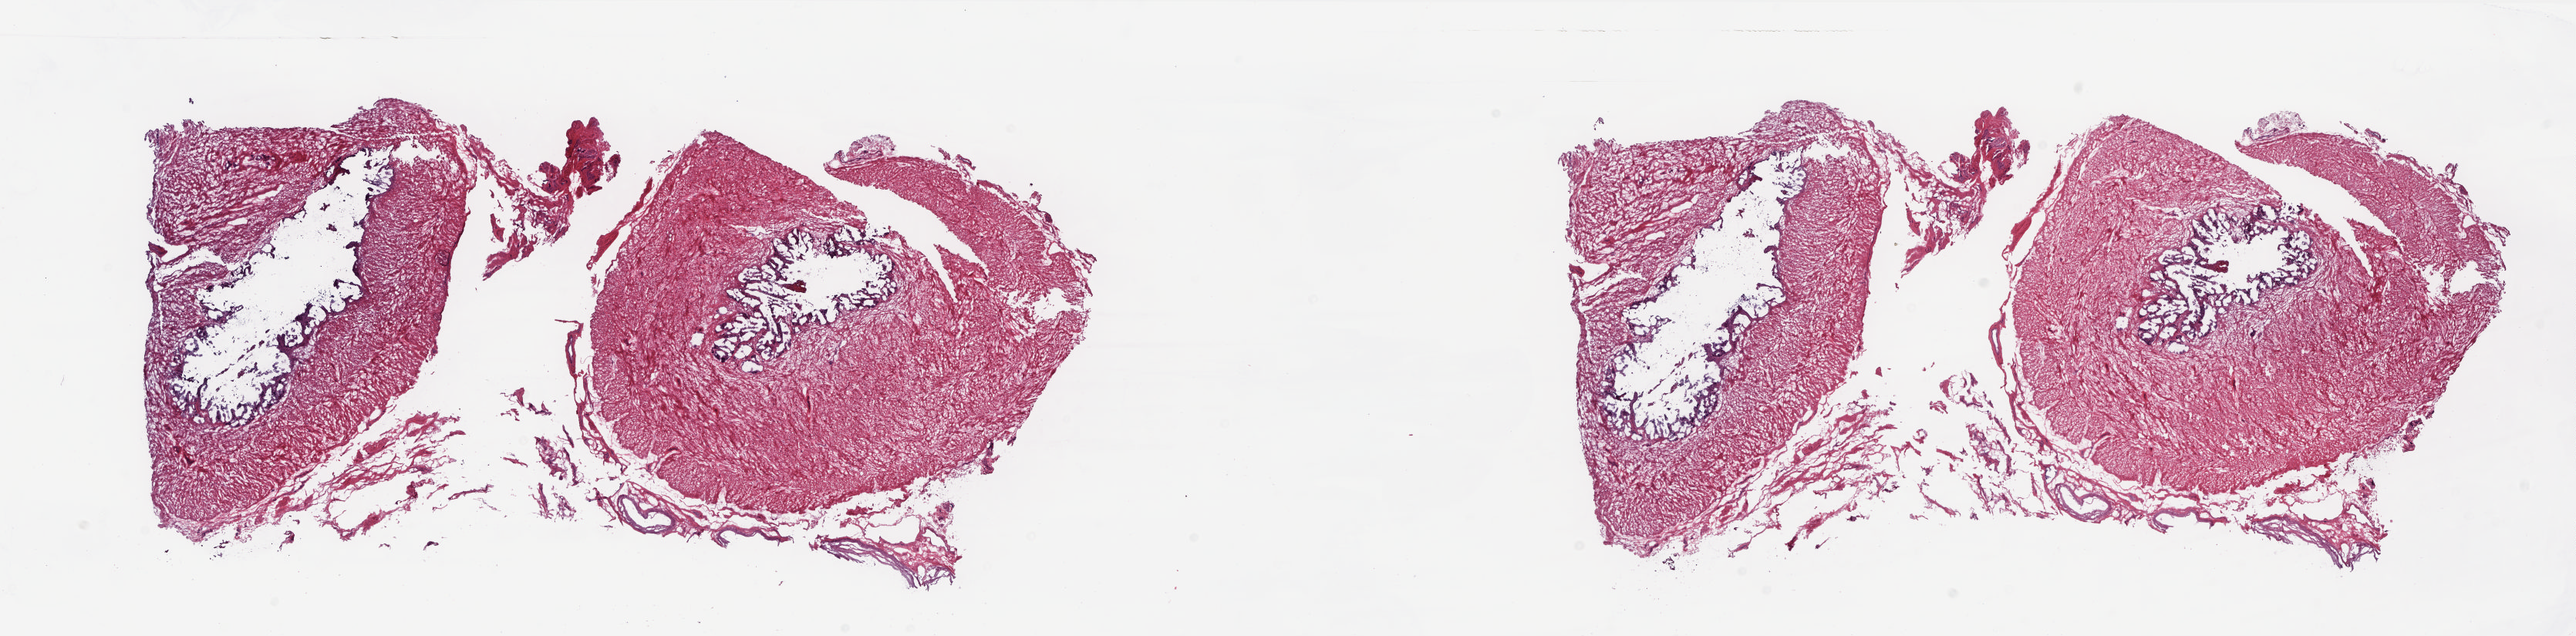
Digitized Hematoxylin and eosin (H&E) stained tissue section (whole slide) — whole scanned area (about 26.9 x 6.7 mm) shown as a low-resolution overview; frozen section from the top of the tissue portion; sample: solid tissue normal (non-tumour tissue), prostate. Patient: male, age at initial diagnosis 72 years. Slide review estimates, as recorded: tumour cells 0%, tumour nuclei 0%, normal cells 100%, stromal cells 0%, necrosis 0%. Inflammatory infiltration, as recorded: lymphocyte infiltration 1%, monocyte infiltration 0%, neutrophil infiltration 0%.
This section: solid tissue normal sample (biorepository sample class). Patient diagnosis: Adenocarcinoma, NOS (prostate gland).